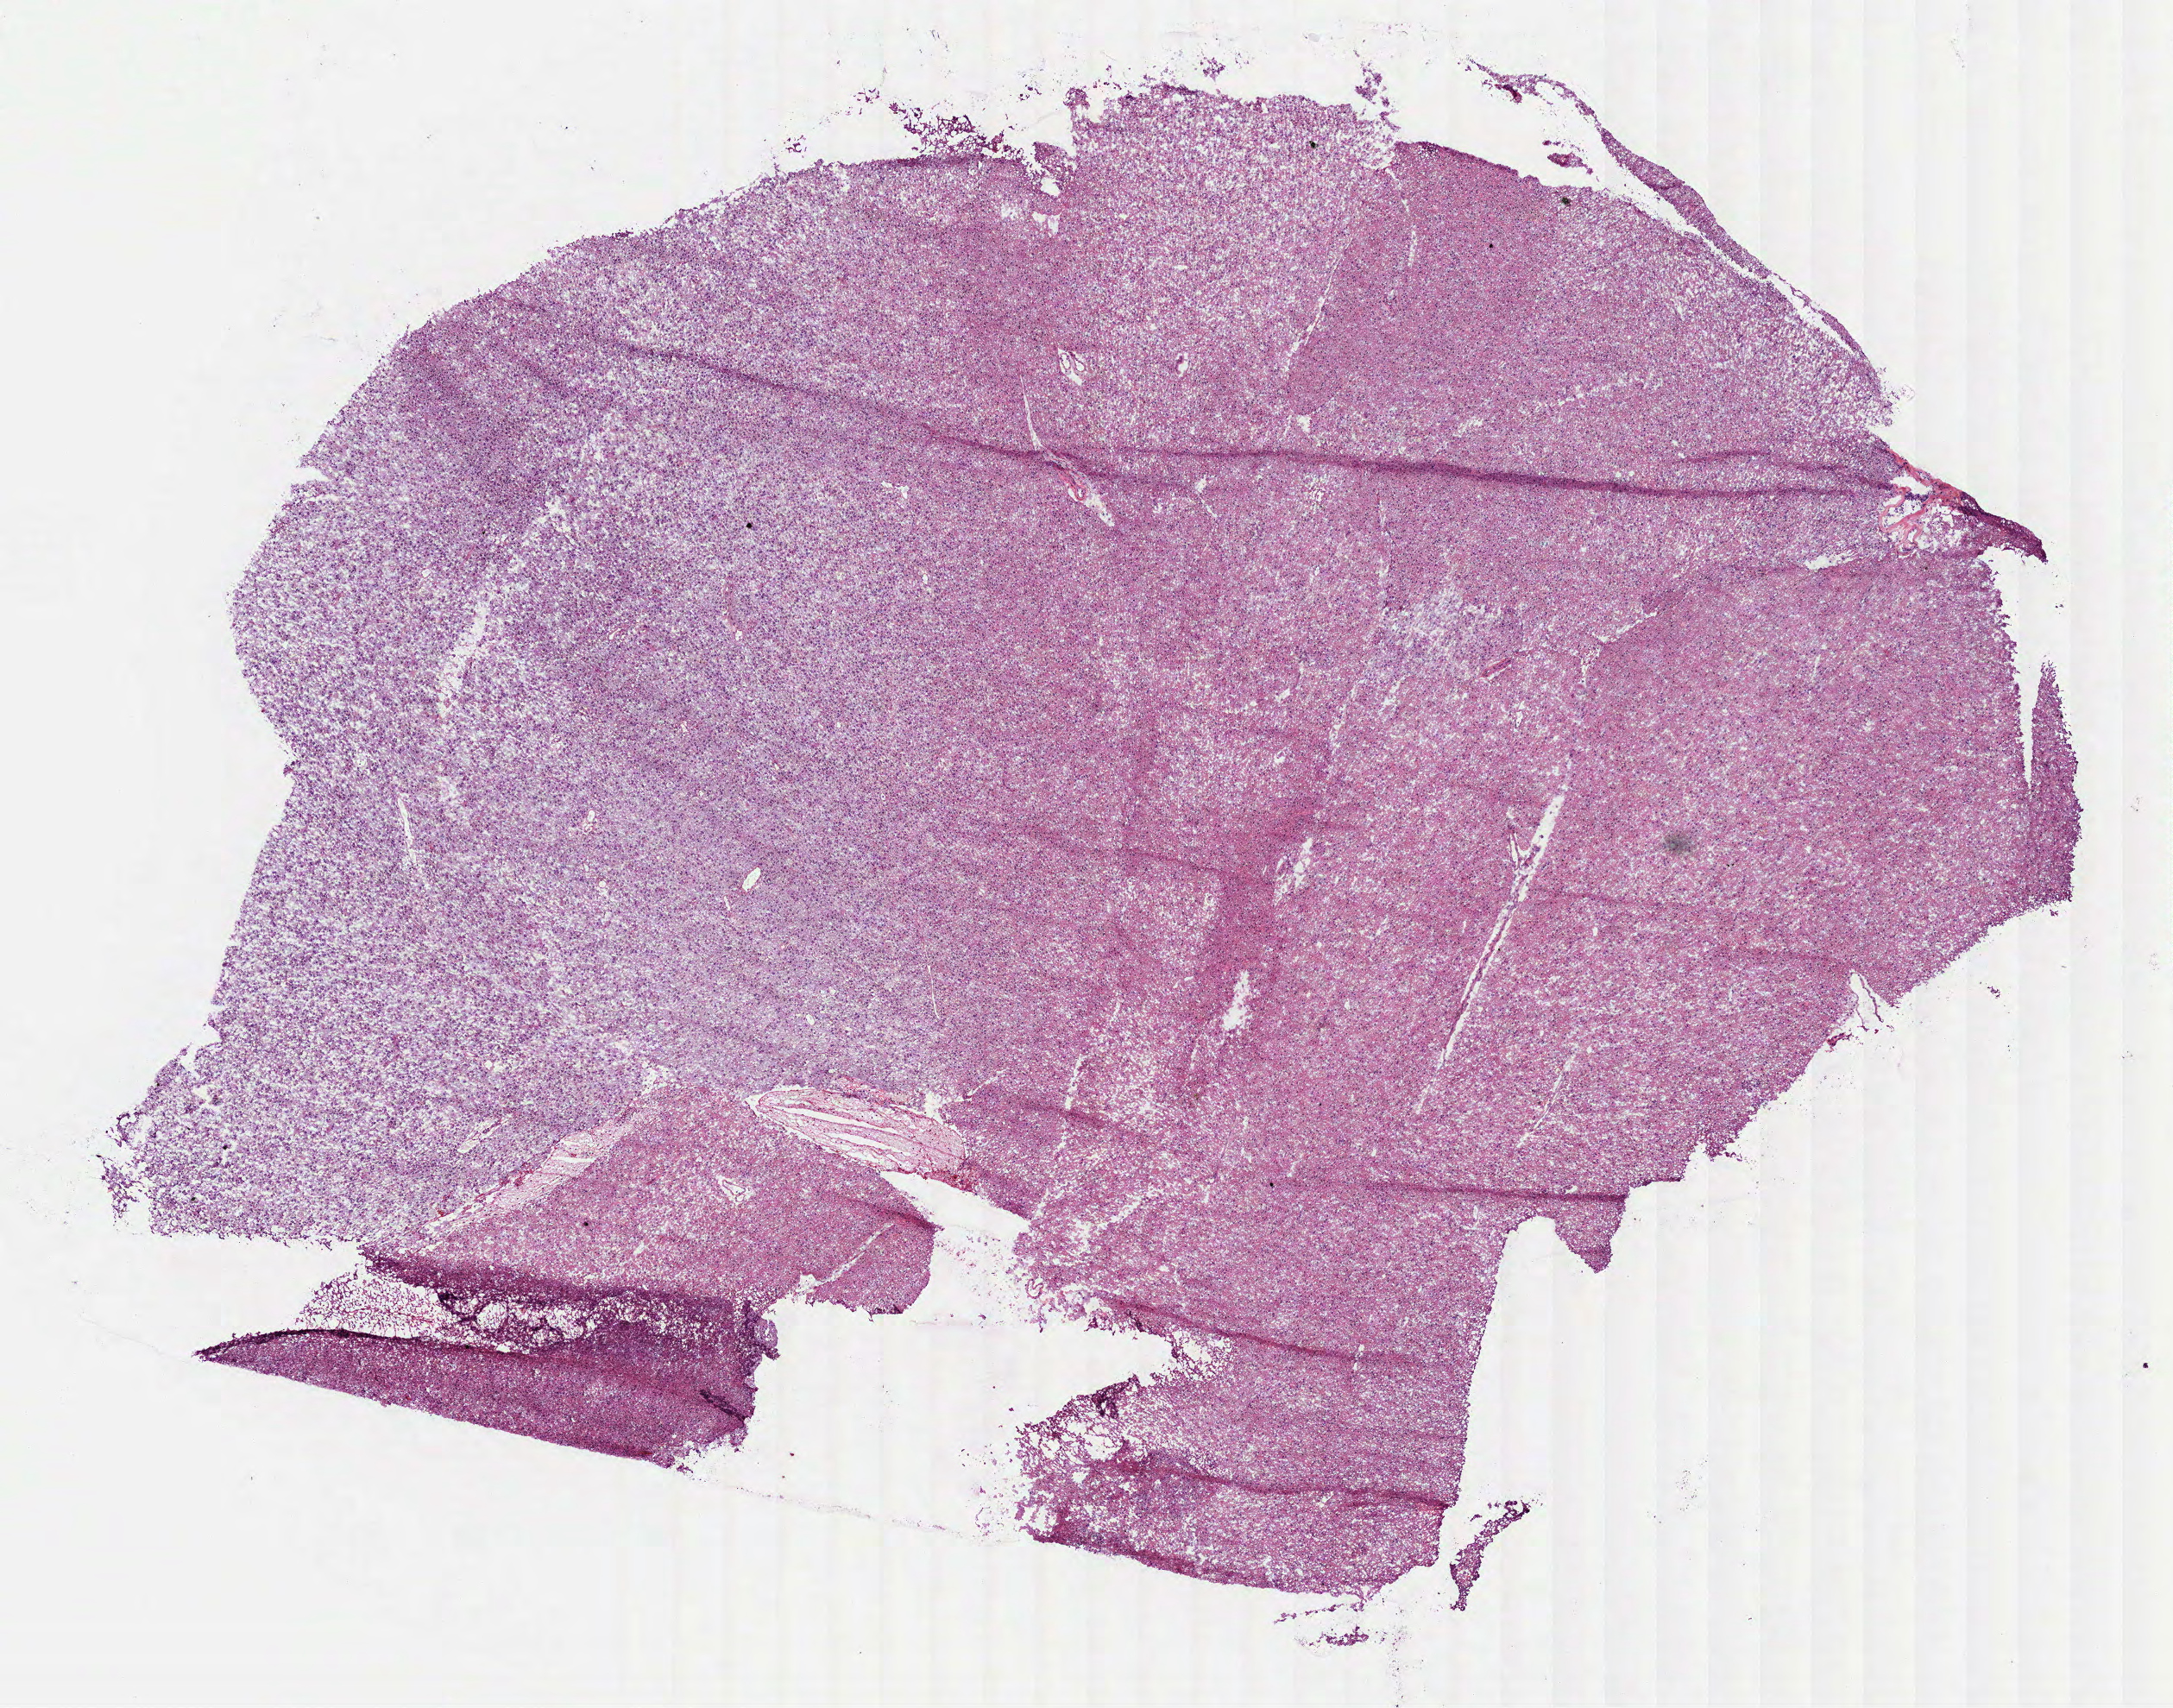
H&E whole-slide image, low-resolution overview of the scanned area, about 10.2 x 8.0 mm (from a 40x scan). Frozen section from the top of the tissue portion. Primary tumour sample from the brain. Patient: female, age at initial diagnosis 53 years.
Histologic diagnosis: Oligodendroglioma, NOS (cerebrum).